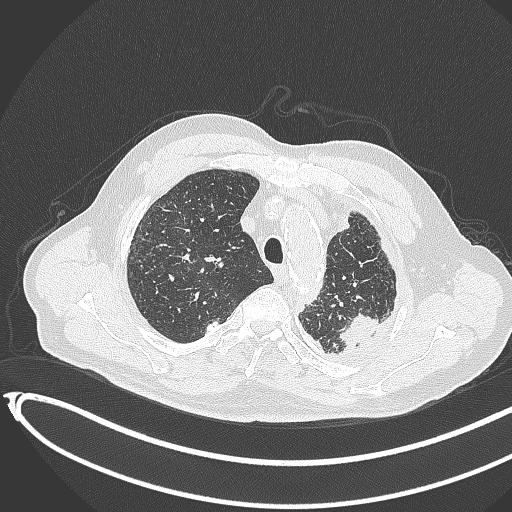
Chest CT, one axial slice. Slice 345 of 451 in the series (ordered by position). Reconstruction kernel B70f. Lung window (W 1500 / L -600 HU). 1 mm slice thickness. 512 × 512 image matrix, field of view 400 × 400 mm. Patient: male, 78 years. Case-level facts recorded for this patient, not image findings: clinical TNM (as recorded): T1c N0 M1.
Annotated regions visible in this slice (bounding box drawn by a radiologist):
- lung tumour (recorded histology: adenocarcinoma): bounding box [x1, y1, x2, y2] px = [330, 313, 380, 349]